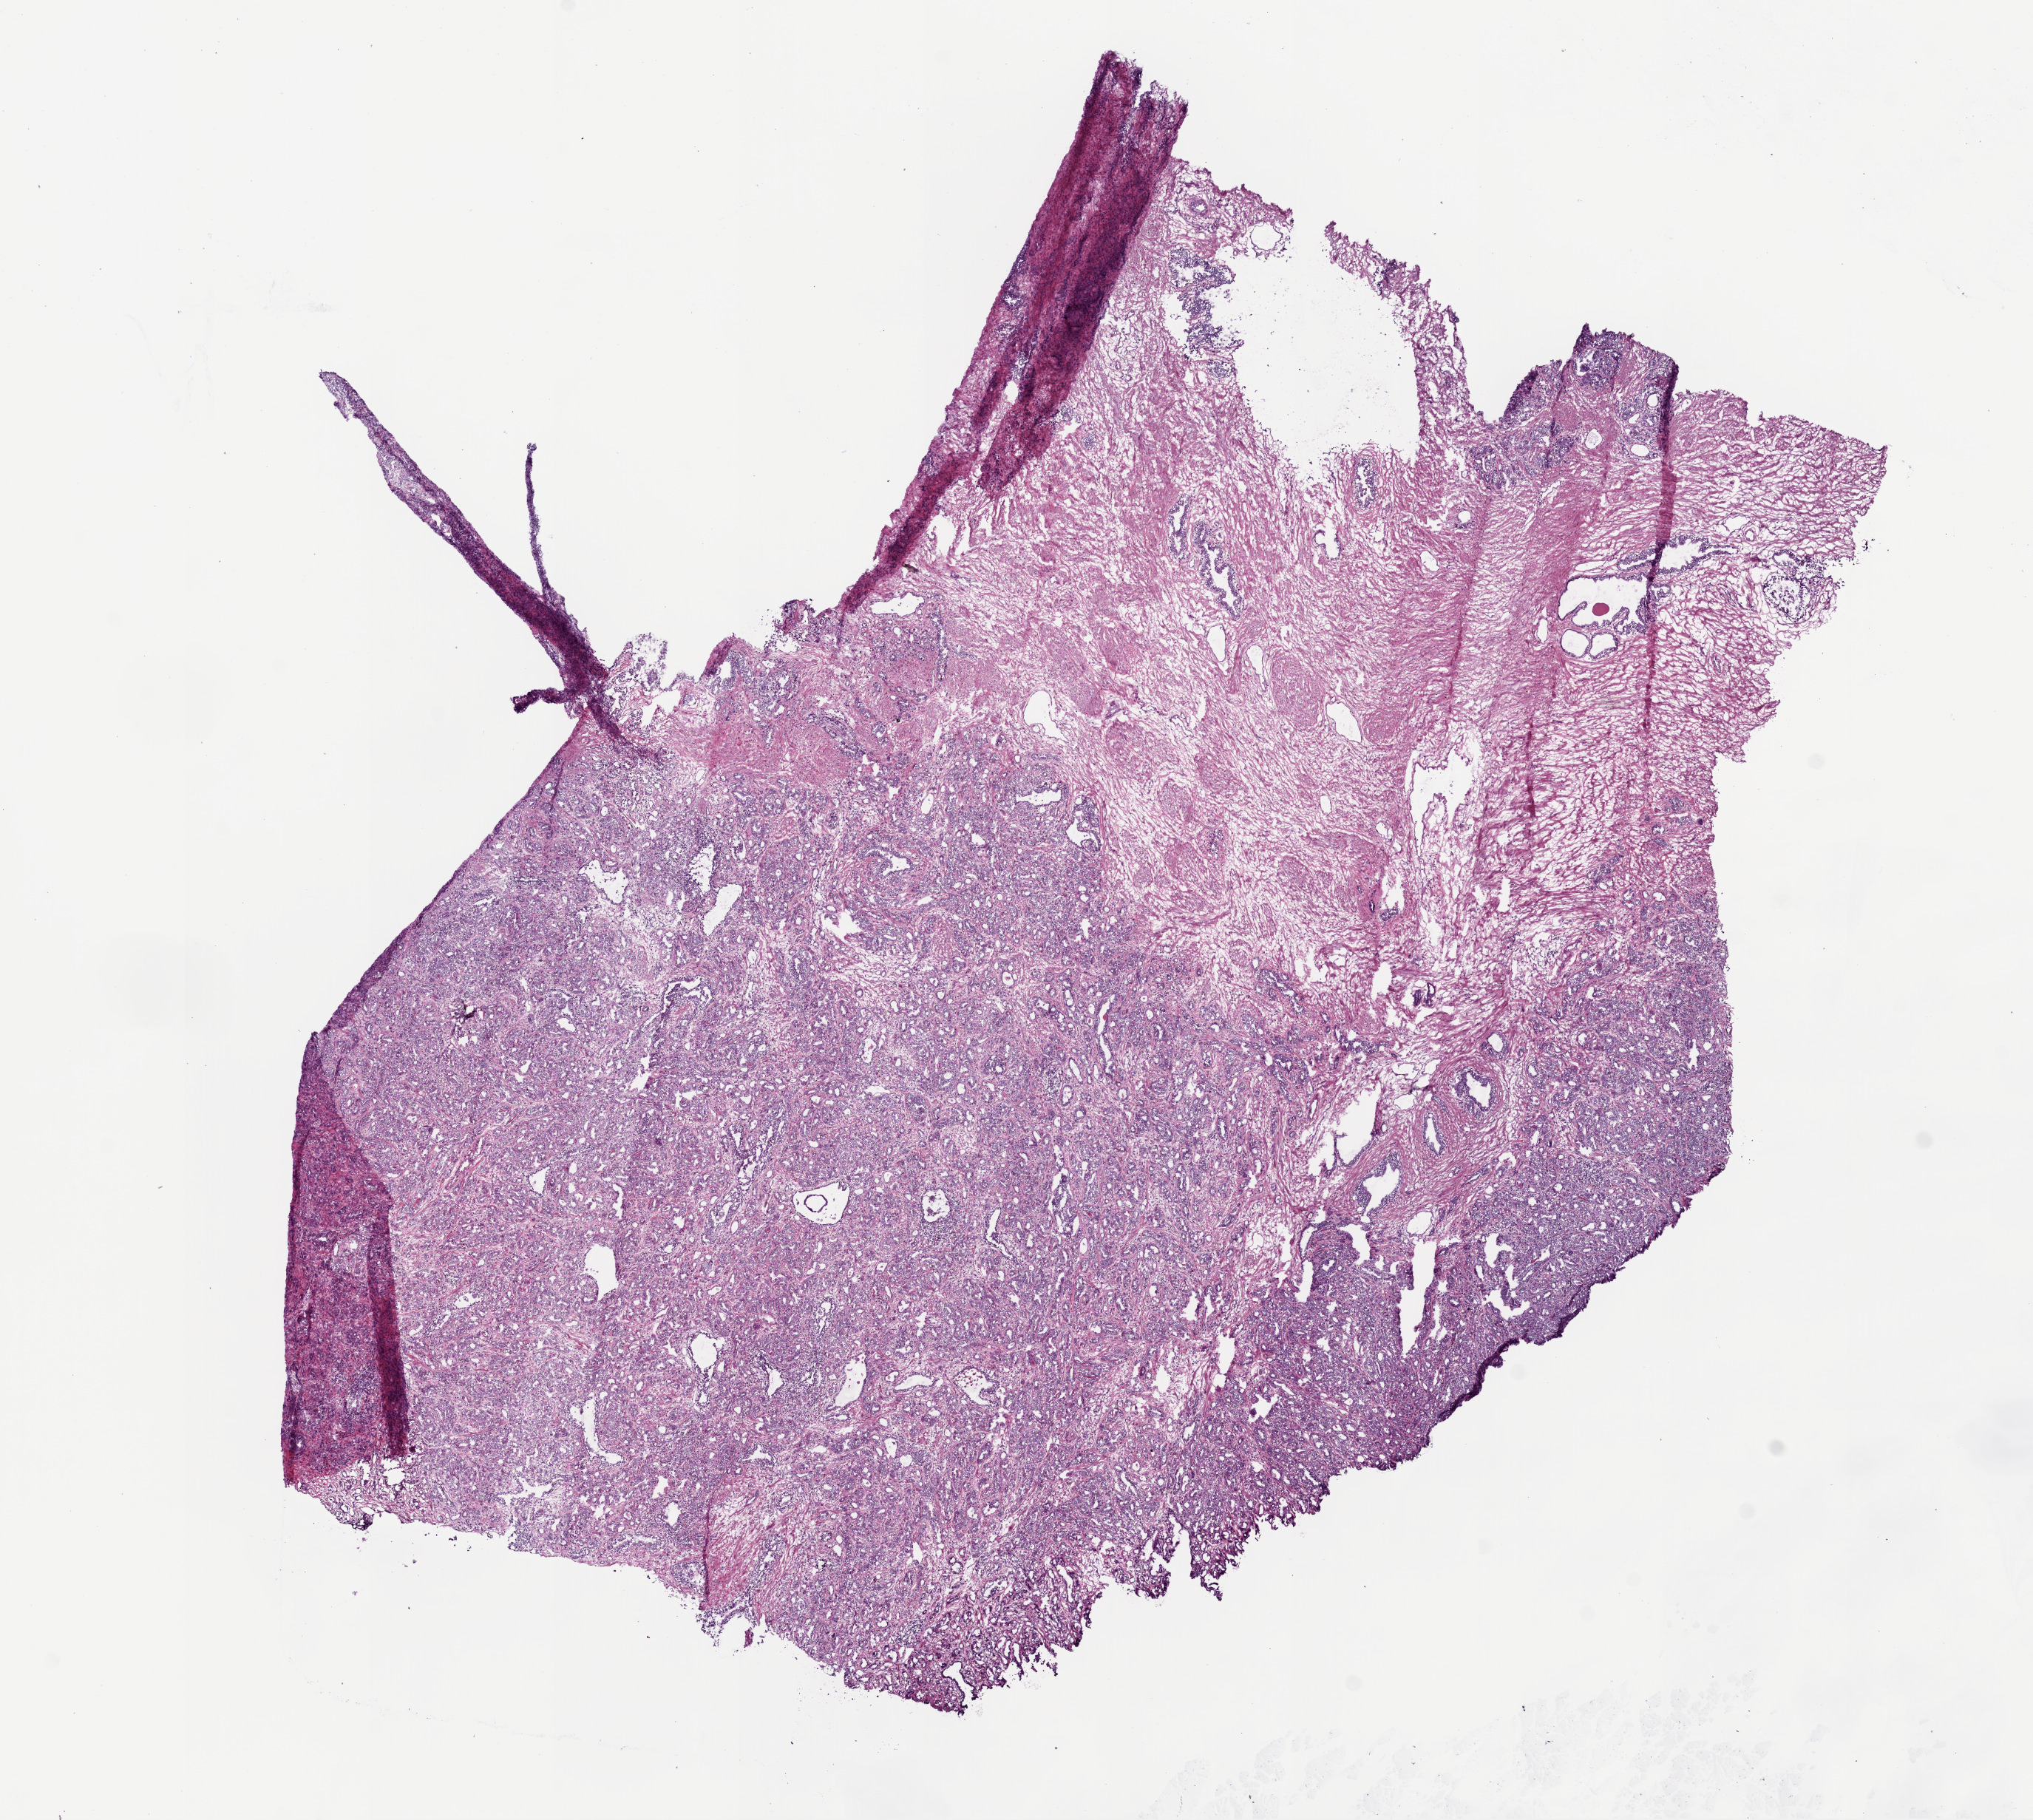
Whole-slide histology image, H&E-stained — low-resolution overview of the scanned area, about 11.0 x 9.9 mm (acquisition: 20x scan). Frozen section from the bottom of the tissue portion. Sample: primary tumour, prostate. Male patient; age at initial diagnosis 55 years. Gleason score: 7 (4+3). Composition of this section per pathologist review: tumour cells 65%, tumour nuclei 75%, normal cells 10%, stromal cells 25%, necrosis 0%. Infiltration values recorded for this section: lymphocyte infiltration 1%, monocyte infiltration 0%, neutrophil infiltration 0%.
Histologic diagnosis: Acinar cell carcinoma (prostate gland). Lymph nodes positive (case pathology): 0 of 11 examined. Laterality: bilateral.